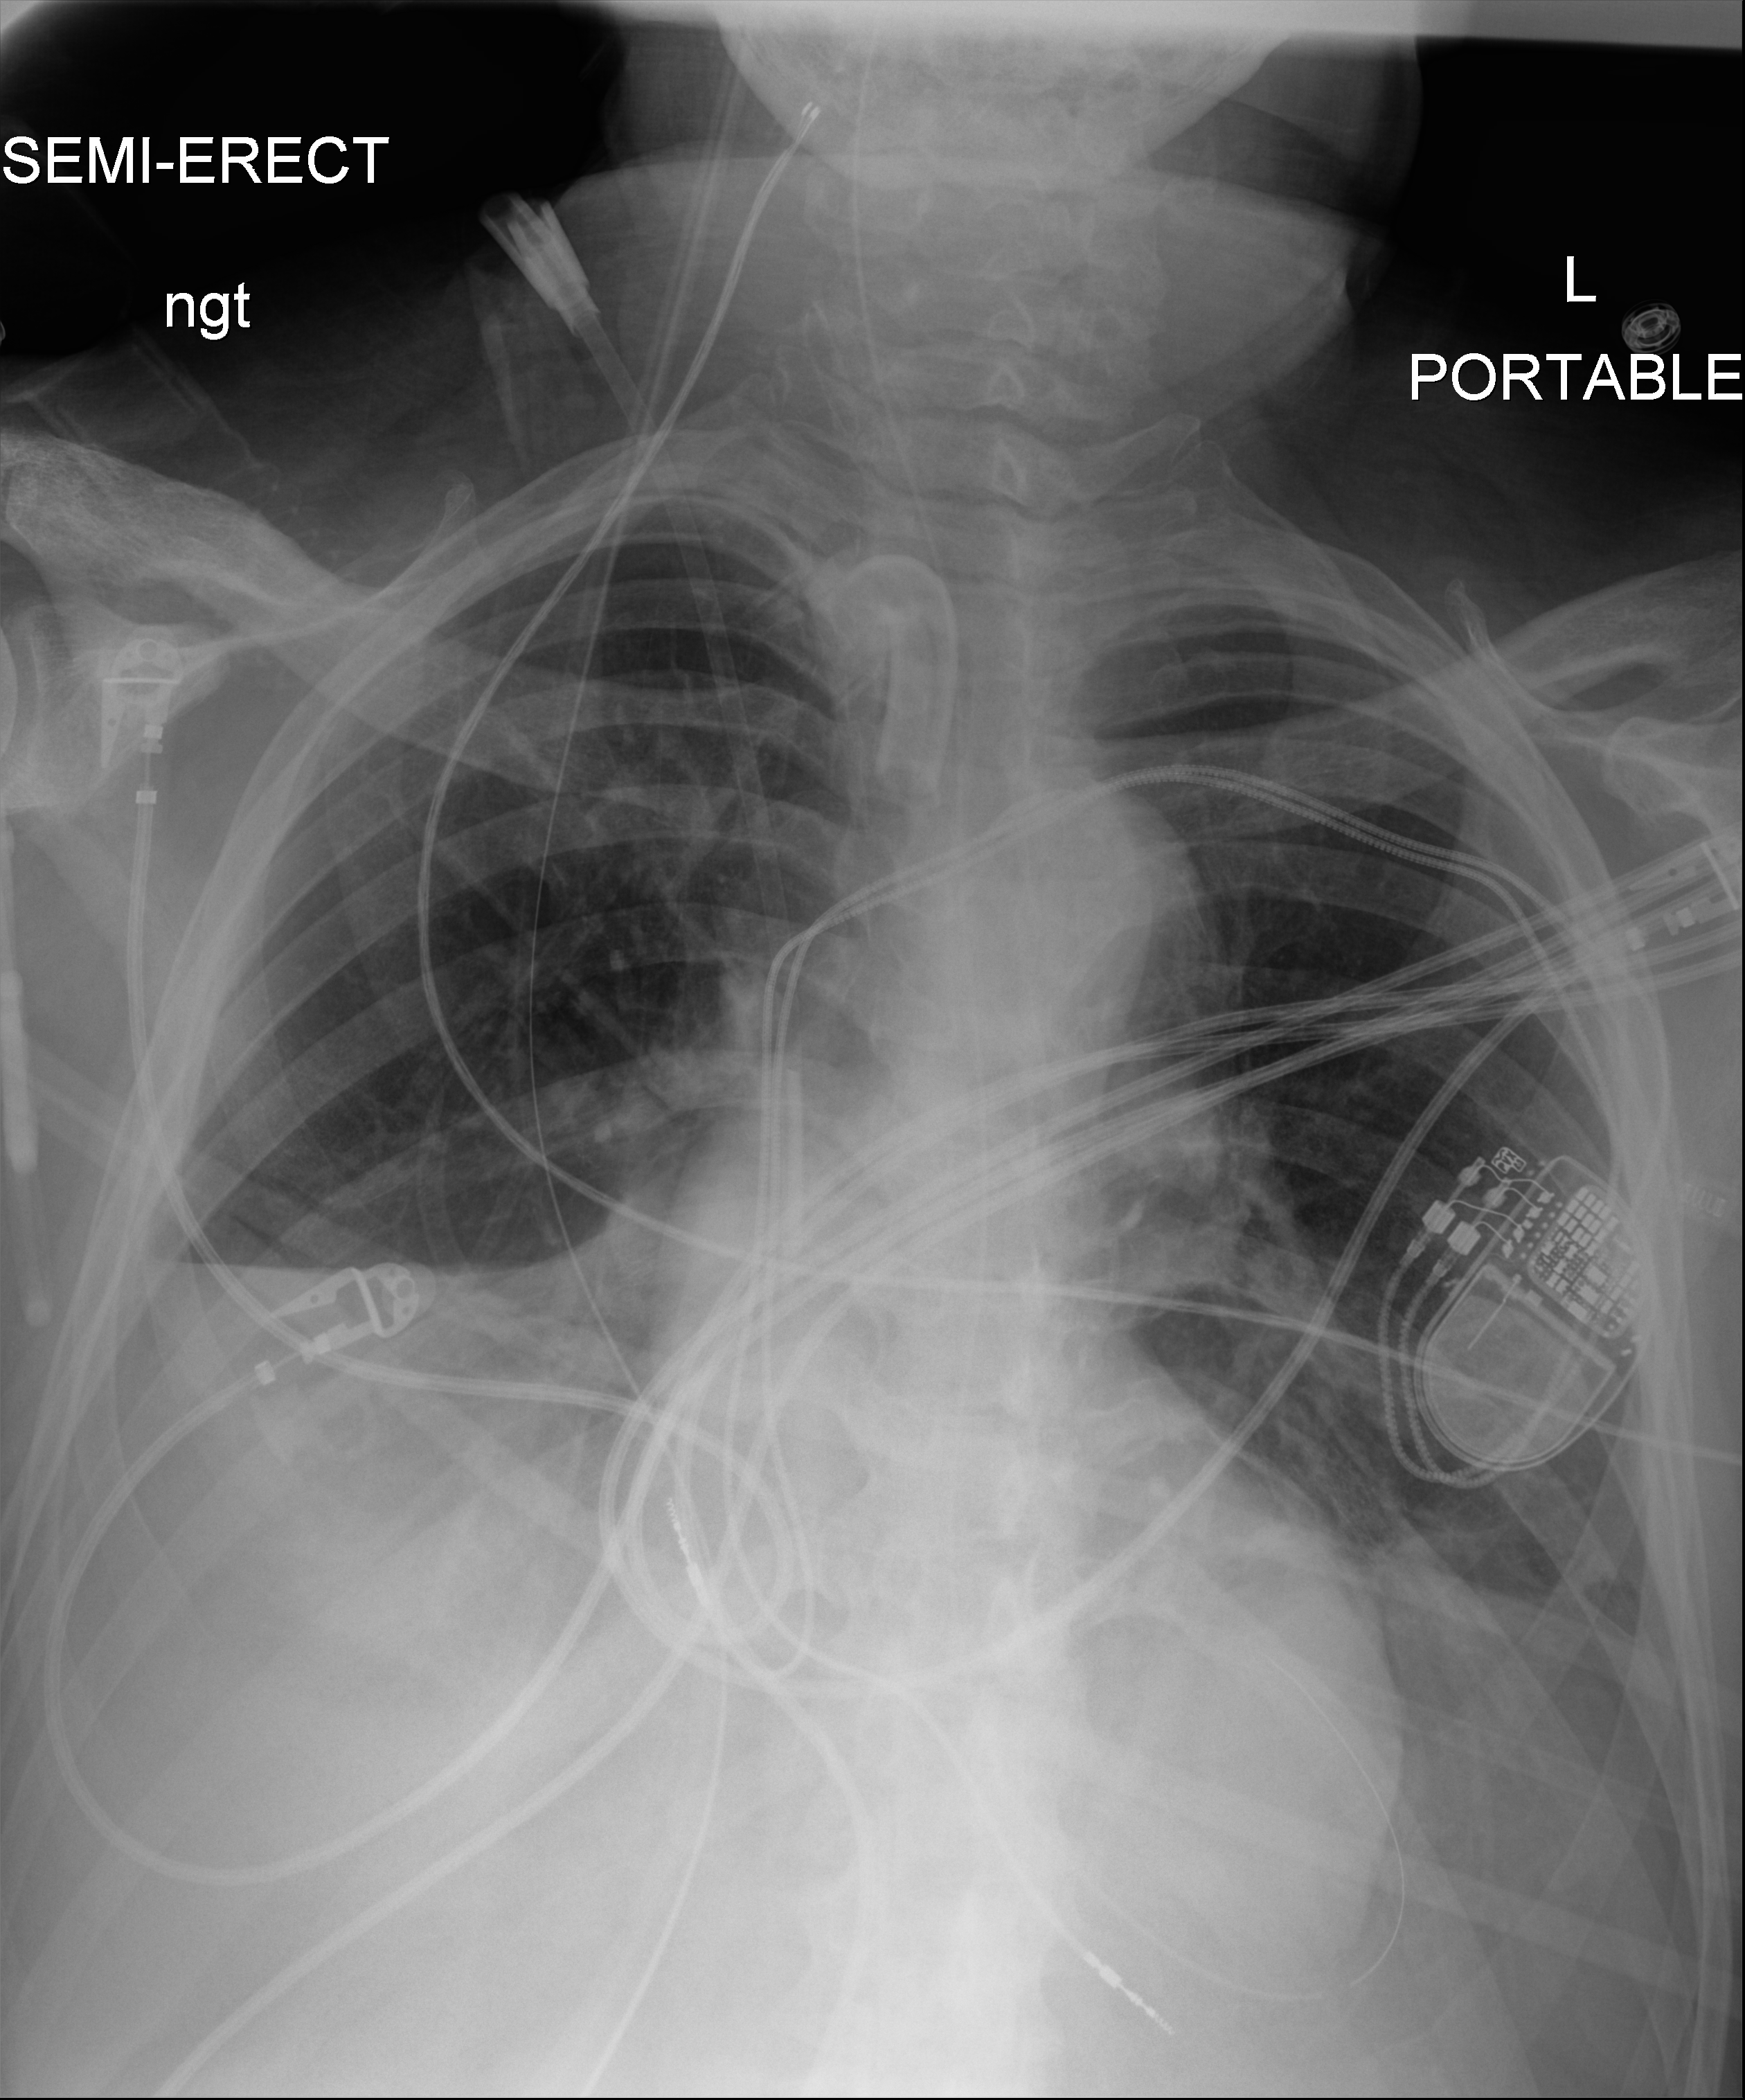
Portable chest radiograph. Patient hospitalised with COVID-19; male, aged 60–74 years.
Admission-level facts for this patient (not findings on this image; timing relative to this image not recorded): admitted to intensive care during this hospital stay: yes; mechanically ventilated during this hospital stay: yes.